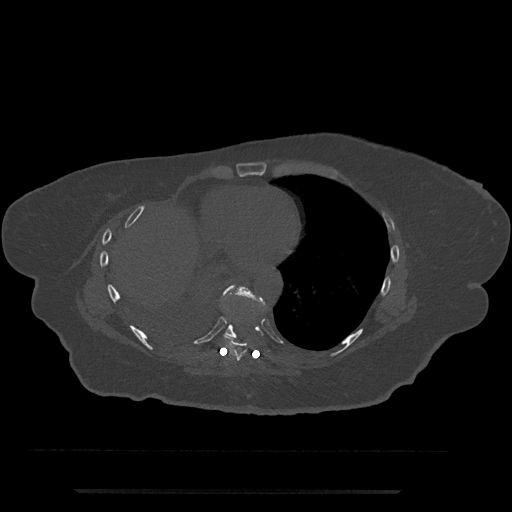
CT including the spine, one axial slice; slice 371 of 797 in the series (ordered by position); reconstruction kernel Br40s/3; 120 kVp; bone window (W 1800 / L 400 HU); 0.5 mm slice thickness; 512 × 512 image matrix, field of view 440 × 440 mm. Patient: female, 51 years. From the clinical record (not read from this slice): primary cancer: neuro; vertebrae with lytic lesions (as recorded): T8.
Annotated regions visible in this slice (semi-automatic segmentation, software-assisted and operator-edited):
- T8 vertebra: box from (x=223, y=333) to (x=248, y=361) px
- T9 vertebra: (x=218, y=285)–(x=266, y=339)